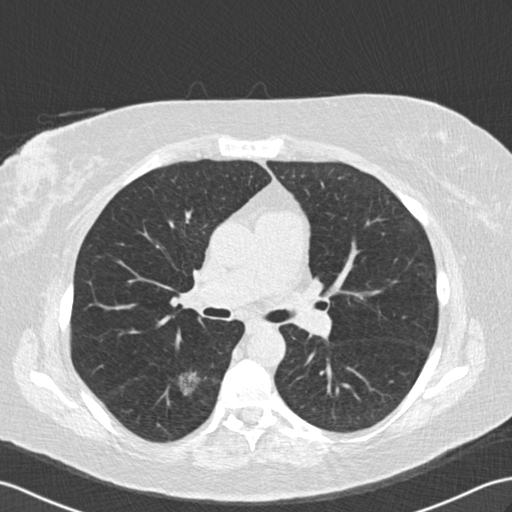
Low-dose screening chest CT, one axial slice; slice 93 of 154 in the series (ordered by position); reconstruction kernel B30f; 120 kVp; lung window (W 1500 / L -600 HU); 2 mm slice thickness; 512 × 512 image matrix, field of view 352 × 352 mm.
Structures marked on this image (manually delineated by an expert):
- lesion 1 (tumor, lower lobe of right lung): bounding box (x1, y1, x2, y2) in pixels: (179, 370, 200, 396)